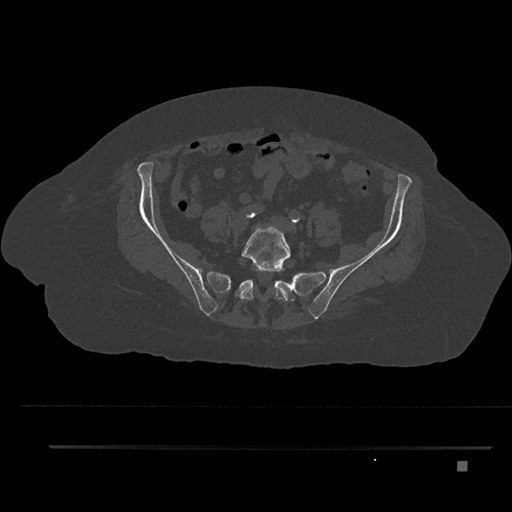
CT including the spine, one axial slice. Position 25 of 797 along the scan axis. Reconstruction kernel Br40s/3. 120 kVp. Bone window (W 1800 / L 400 HU). 0.5 mm slice thickness. 512 × 512 image matrix, field of view 437 × 437 mm. Female patient, age 76 years. Case-level facts recorded for this patient, not image findings: primary cancer: lung; vertebrae with lytic lesions (as recorded): T11, L3.
Outlined on this slice (semi-automatic segmentation, software-assisted and operator-edited):
- L5 vertebra: bounding box [x1, y1, x2, y2] px = [240, 224, 291, 302]